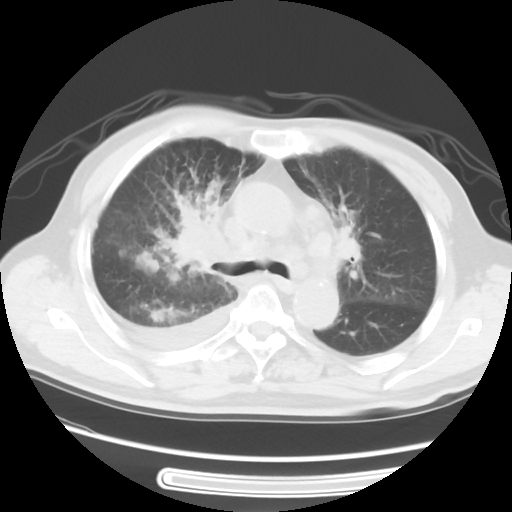
Chest CT, one axial slice; position 36 of 56 along the scan axis; 120 kVp; lung window (W 1500 / L -600 HU); 5 mm slice thickness; 512 × 512 image matrix, field of view 360 × 360 mm. Male patient, age 77 years. Case-level facts recorded for this patient, not image findings: clinical TNM (as recorded): T3 N3 M1b.
Annotated regions visible in this slice (rectangle marked by the reading radiologist):
- lung tumour (recorded histology: small cell carcinoma): bounding box <158,189,237,274> (left, top, right, bottom; pixels)